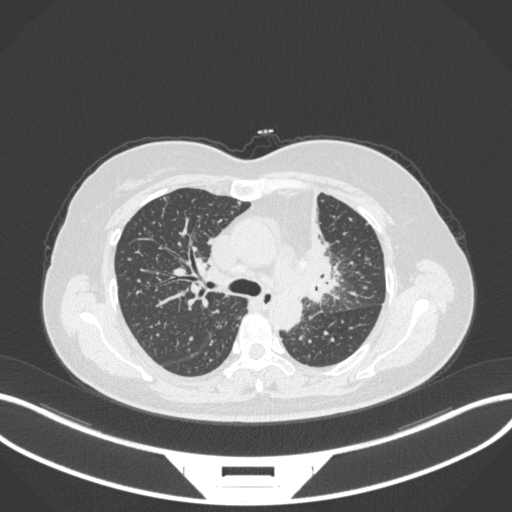
Chest CT, one axial slice. Slice 222 of 348 in the series (ordered by position). Reconstruction kernel B31f. 120 kVp. Lung window (W 1500 / L -600 HU). 1 mm slice thickness. 512 × 512 image matrix, field of view 400 × 400 mm. Female patient, age 49 years. From the clinical record (not read from this slice): clinical TNM (as recorded): T1c N0 M1.
Outlined on this slice (bounding box drawn by a radiologist):
- lung tumour (recorded histology: adenocarcinoma): bounding box <298,185,346,309> (left, top, right, bottom; pixels)